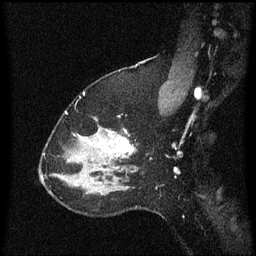
Breast MRI (dynamic contrast-enhanced), one sagittal slice; slice 45 of 60 in the series (ordered by position); dynamic contrast-enhanced series, image 2 of 3 at this slice position (ordered by acquisition); 1.5 T; TE 4.2 ms, TR 8.4 ms; 2 mm slice thickness; 256 × 256 image matrix, field of view 200 × 200 mm. Patient: female, 37 years. From the clinical record (not read from this slice): setting: breast cancer imaged before/during neoadjuvant chemotherapy; receptor status: HR-positive, HER2-negative.
Outlined on this slice (semi-automatic segmentation, software-assisted and operator-edited):
- analysis volume of interest (the breast-tissue region the enhancement analysis was run in; not a lesion): bounding box (x1, y1, x2, y2) in pixels: (95, 116, 153, 171)
- tumour enhancement mask (voxels above the 70 % enhancement threshold inside the analysis volume of interest): (116, 136, 135, 155)